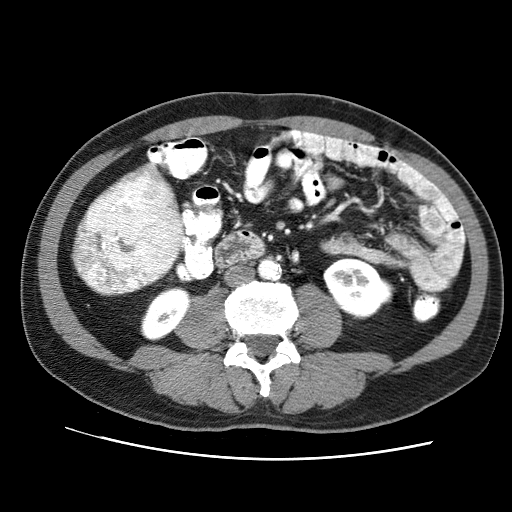
Contrast-enhanced abdominal CT (liver protocol), one axial slice; slice 12 of 71 in the series (ordered by position); reconstruction kernel STANDARD; soft-tissue window (W 400 / L 40 HU); 2.5 mm slice thickness; 512 × 512 image matrix, field of view 360 × 360 mm. Case-level facts recorded for this patient, not image findings: diagnosis: hepatocellular carcinoma (patient treated with transarterial chemoembolisation; whether this scan precedes or follows treatment is not stated here); TNM stage (as recorded): Stage-II; Child-Pugh class: A; tumour nodularity: multinodular.
Annotated regions visible in this slice (semi-automatically segmented with operator editing):
- liver parenchyma outside the tumour (the mass and vessels are separate outlines, so this box may not span the whole liver): bounding box <73,175,186,293> (left, top, right, bottom; pixels)
- mass: <71,164,185,295>